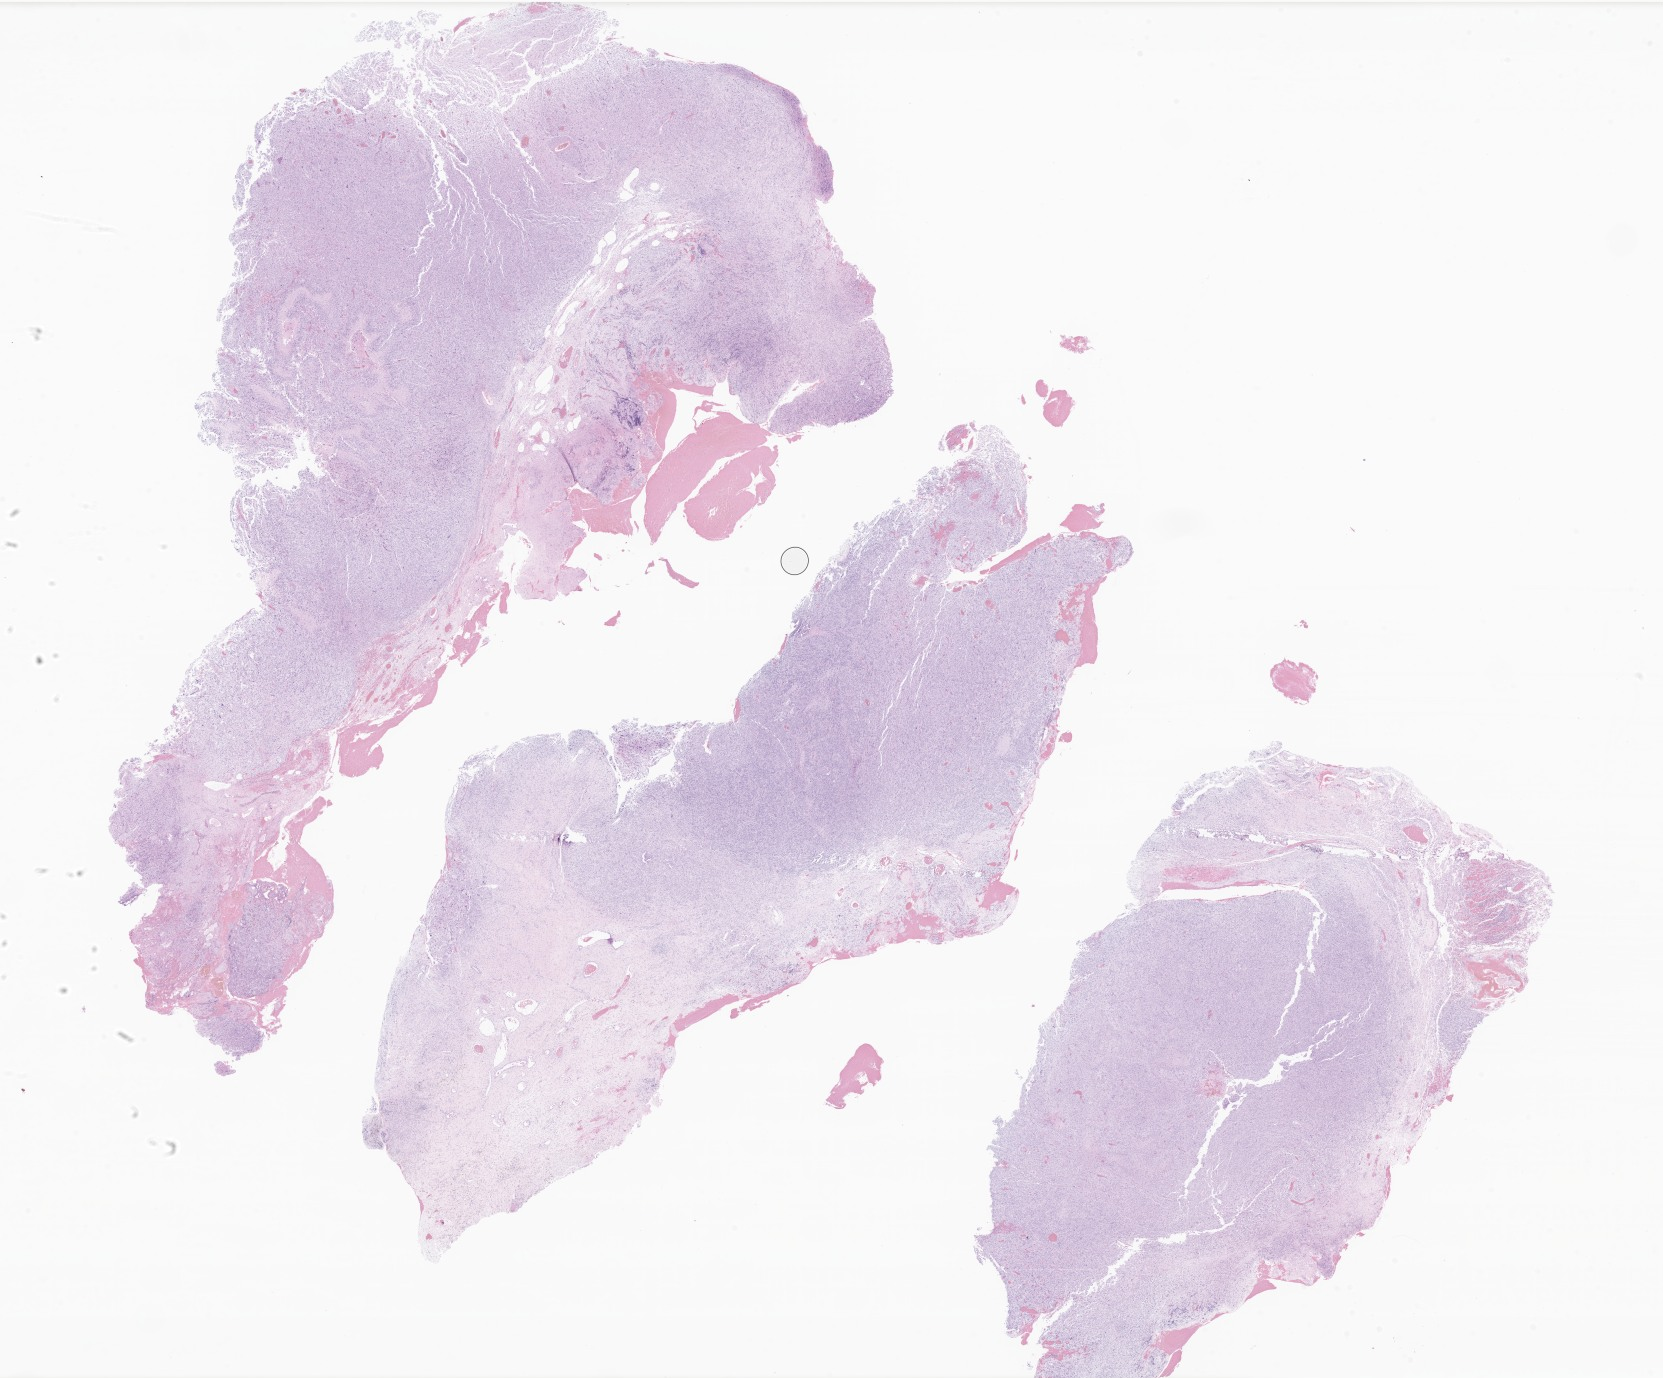
Digitized hematoxylin and eosin (H&E)-stained section of tumor tissue from the brain — shown as a low-resolution overview of the whole scanned area (about 28.0 x 23.2 mm), FFPE section. Patient: male, age 203 months (16 years 11 months).
Diagnosis (ICD-O-3 morphology term): Glioblastoma, NOS.